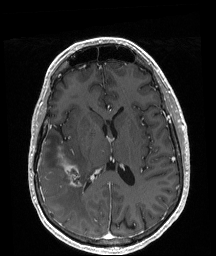
Brain MRI from a brain-tumour surgery series, one axial slice; slice 96 of 208 in the series (ordered by position); T1-weighted post-contrast; 1 mm slice thickness; 216 × 256 image matrix, field of view 211 × 250 mm. Case-level facts recorded for this patient, not image findings: histopathology: Astrocytoma; WHO grade: 4; IDH mutation: yes; tumour location: Right Temporal.
Annotated regions visible in this slice (outlined manually by an expert reader):
- tumour: bounding box (x1, y1, x2, y2) in pixels: (58, 147, 80, 187)